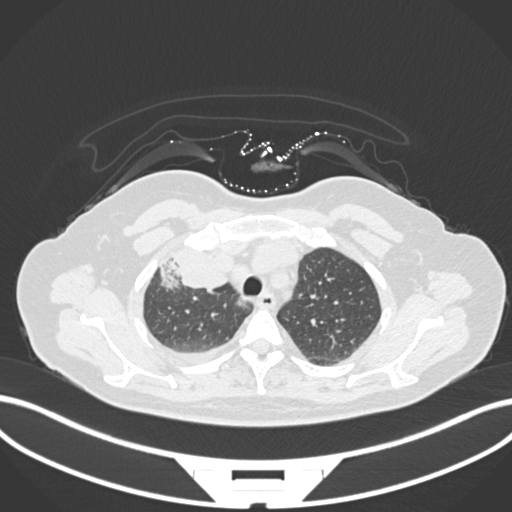
Chest CT, one axial slice; position 132 of 172 along the scan axis; reconstruction kernel B30f; lung window (W 1500 / L -600 HU); 512 × 512 image matrix, field of view 400 × 400 mm. Female patient, age 52 years. Case-level facts recorded for this patient, not image findings: clinical TNM (as recorded): T3 N1 M1.
Annotated regions visible in this slice (bounding box drawn by a radiologist):
- lung tumour (recorded histology: adenocarcinoma): box from (x=157, y=251) to (x=230, y=291) px